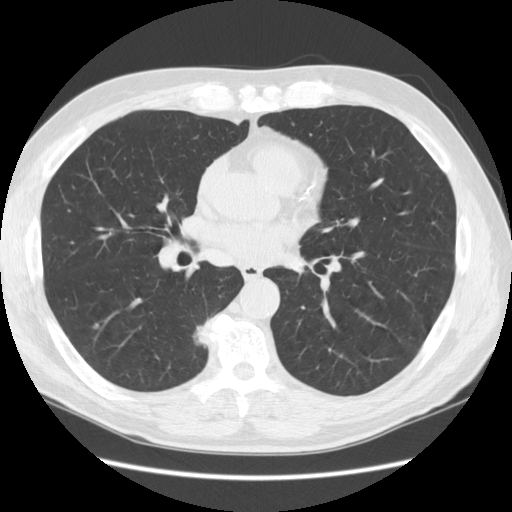
Low-dose screening chest CT, one axial slice. Position 66 of 133 along the scan axis. 120 kVp. Lung window (W 1500 / L -600 HU). 512 × 512 image matrix, field of view 370 × 370 mm.
Annotated regions visible in this slice (outlined manually by an expert reader):
- lesion 1 (tumor, lower lobe of right lung): bounding box (x1, y1, x2, y2) in pixels: (191, 318, 212, 344)